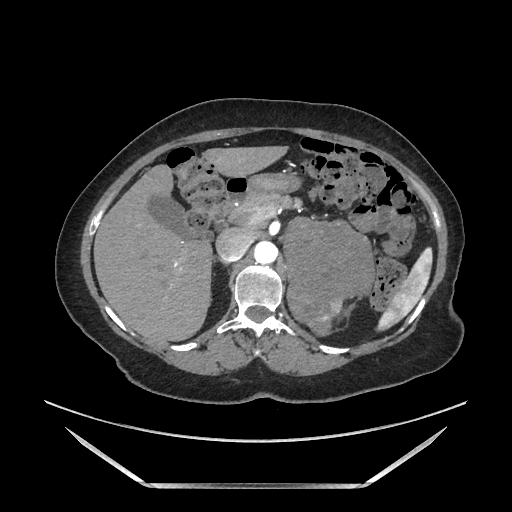
Contrast-enhanced abdominal CT, one axial slice; slice 109 of 205 in the series (ordered by position); soft-tissue window (W 400 / L 40 HU); 1.25 mm slice thickness; 512 × 512 image matrix, field of view 440 × 440 mm. Female patient. From the clinical record (not read from this slice): diagnosis: adrenocortical carcinoma; tumour side: left adrenal; tumour size at pathology: 12.5 cm; Ki-67 index: 39 %.
Outlined on this slice (semi-automatically segmented with operator editing):
- mass: bounding box [x1, y1, x2, y2] px = [287, 222, 370, 335]